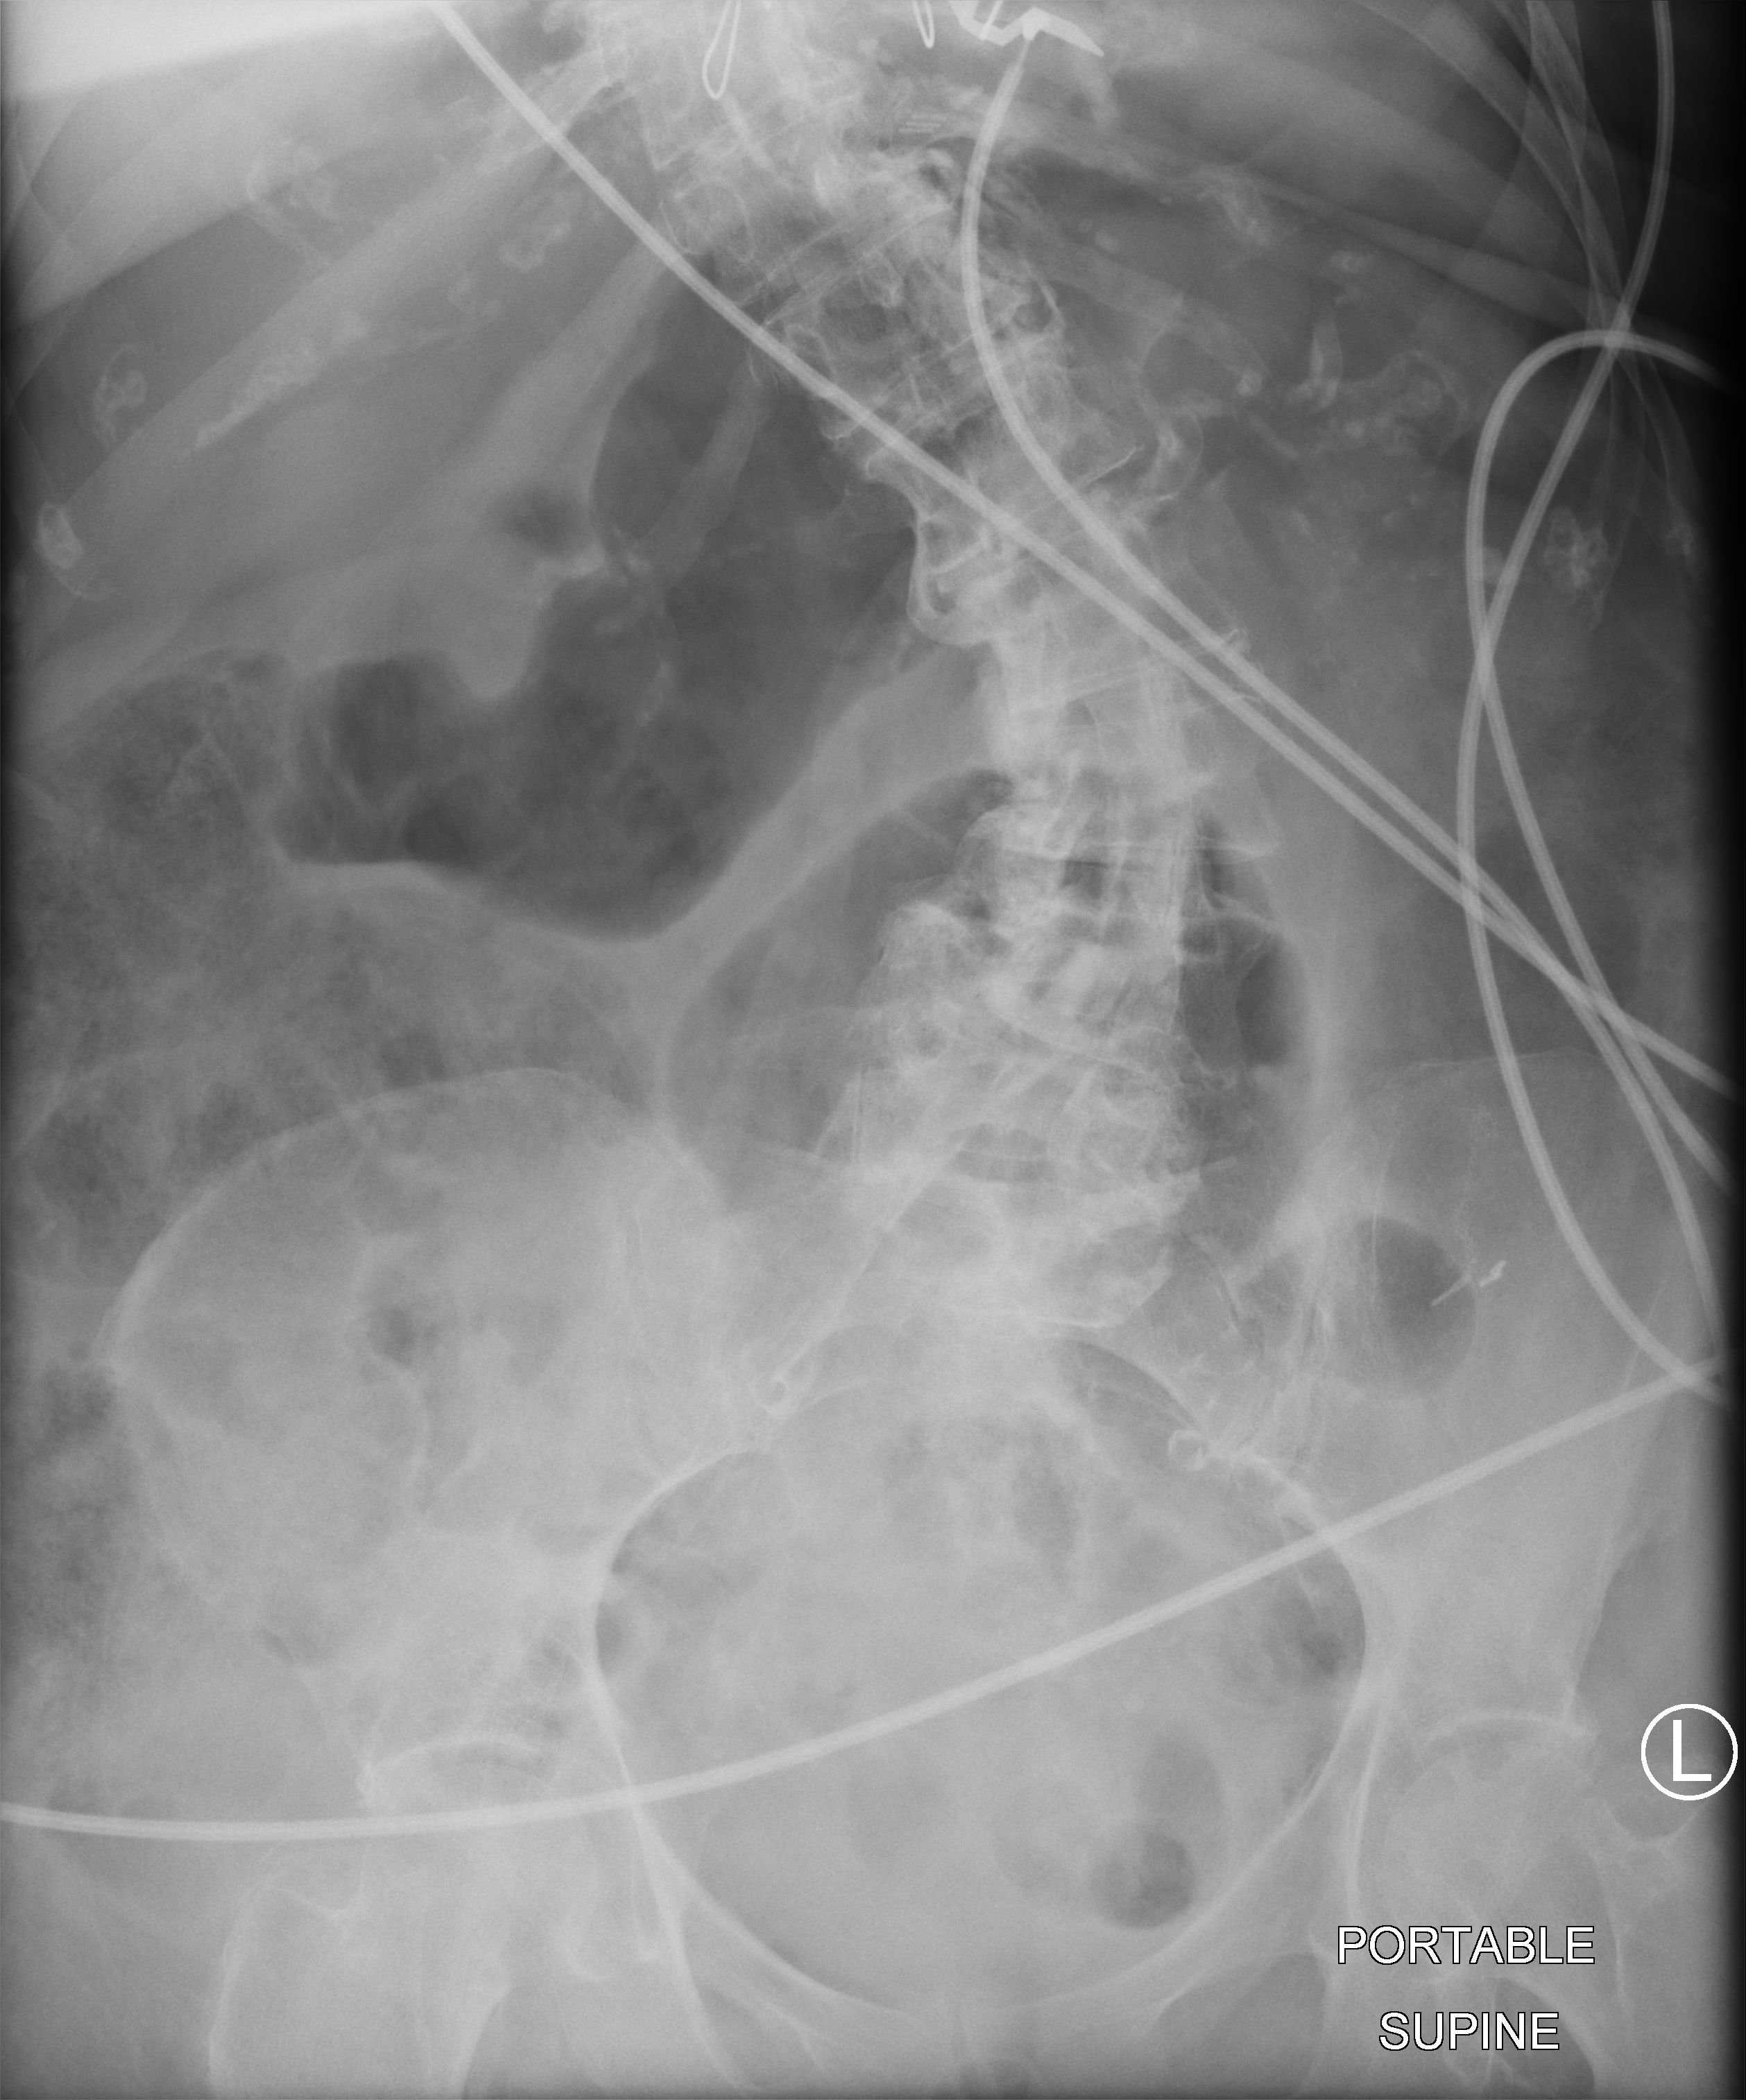
Bedside abdomen radiograph (computed radiography); anteroposterior (AP) projection. Patient hospitalised with COVID-19; female, aged 75–90 years.
Admission-level facts for this patient (not findings on this image; timing relative to this image not recorded): admitted to intensive care during this hospital stay: no.